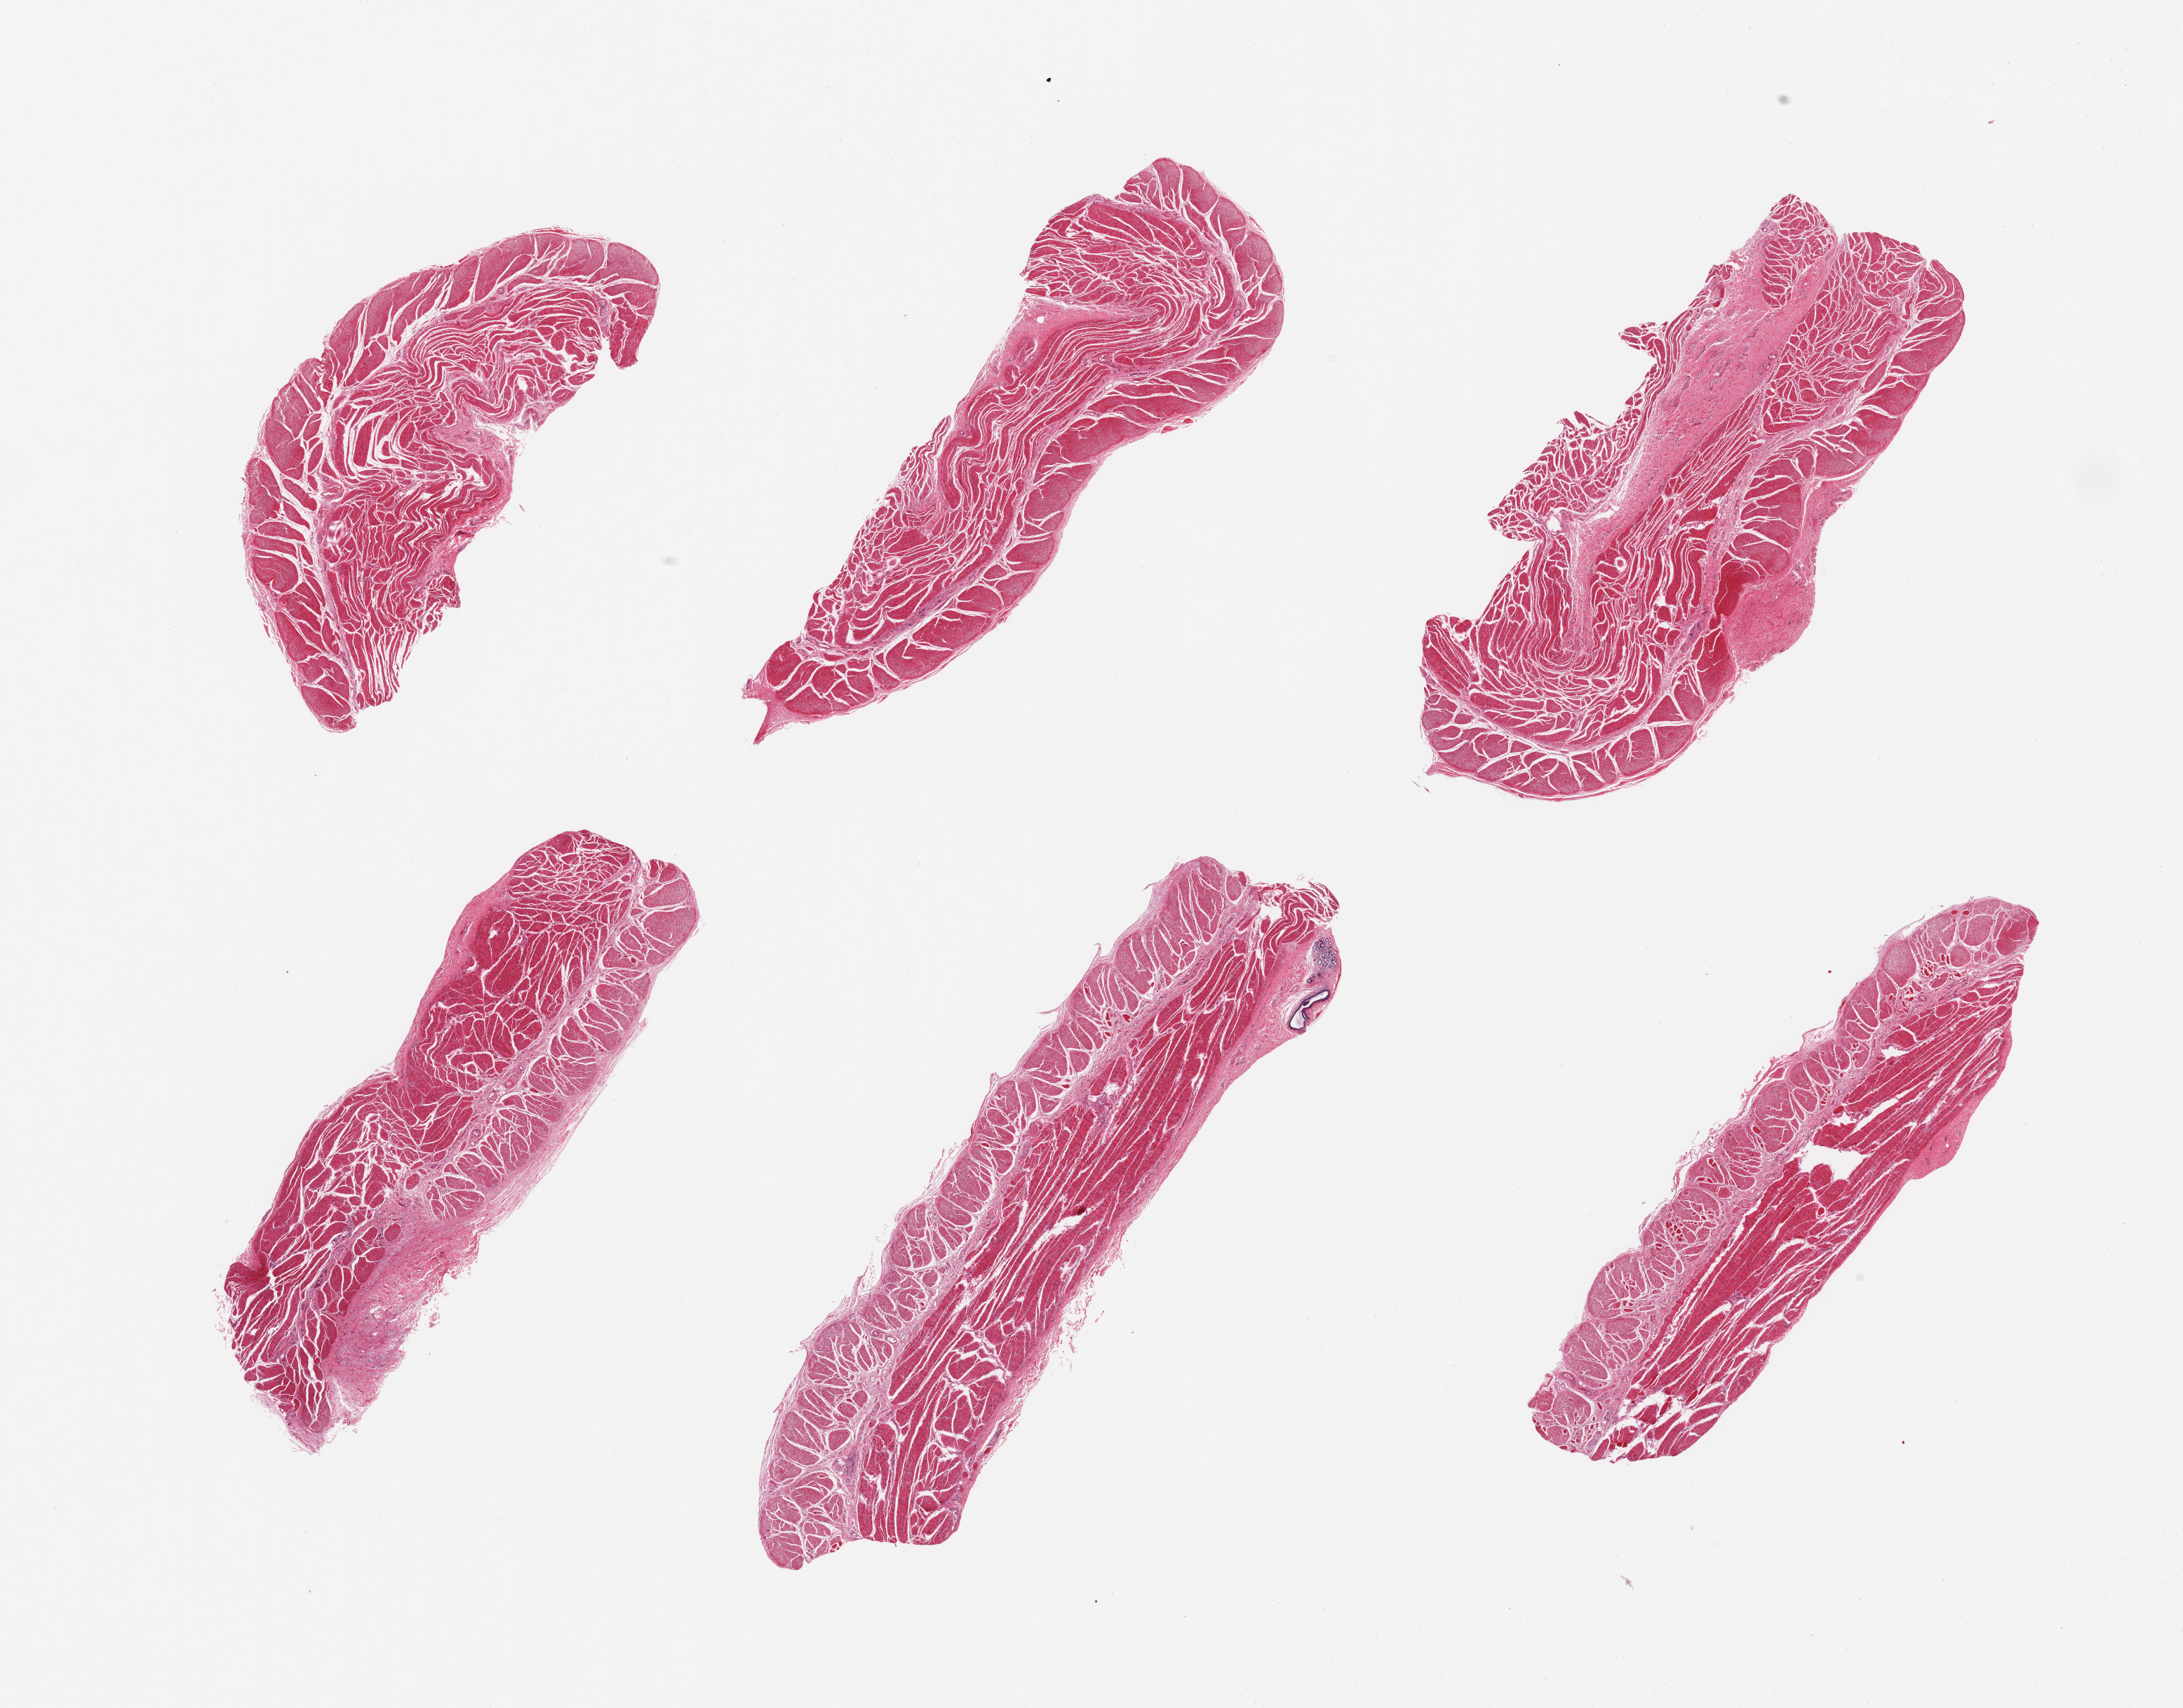
Whole-slide image, hematoxylin and eosin (H&E) stain — shown as a low-resolution overview of the whole scanned area (about 24.6 x 19.3 mm, slide scanned at 20x); PAXgene-fixed paraffin-embedded (PFPE) section; section of esophageal muscle (target tissue); donor tissue sample. Donor: male.
Pathologist's review note for this sample: 6 pieces; admixture with skeletal muscle; specimen taken too proximally.